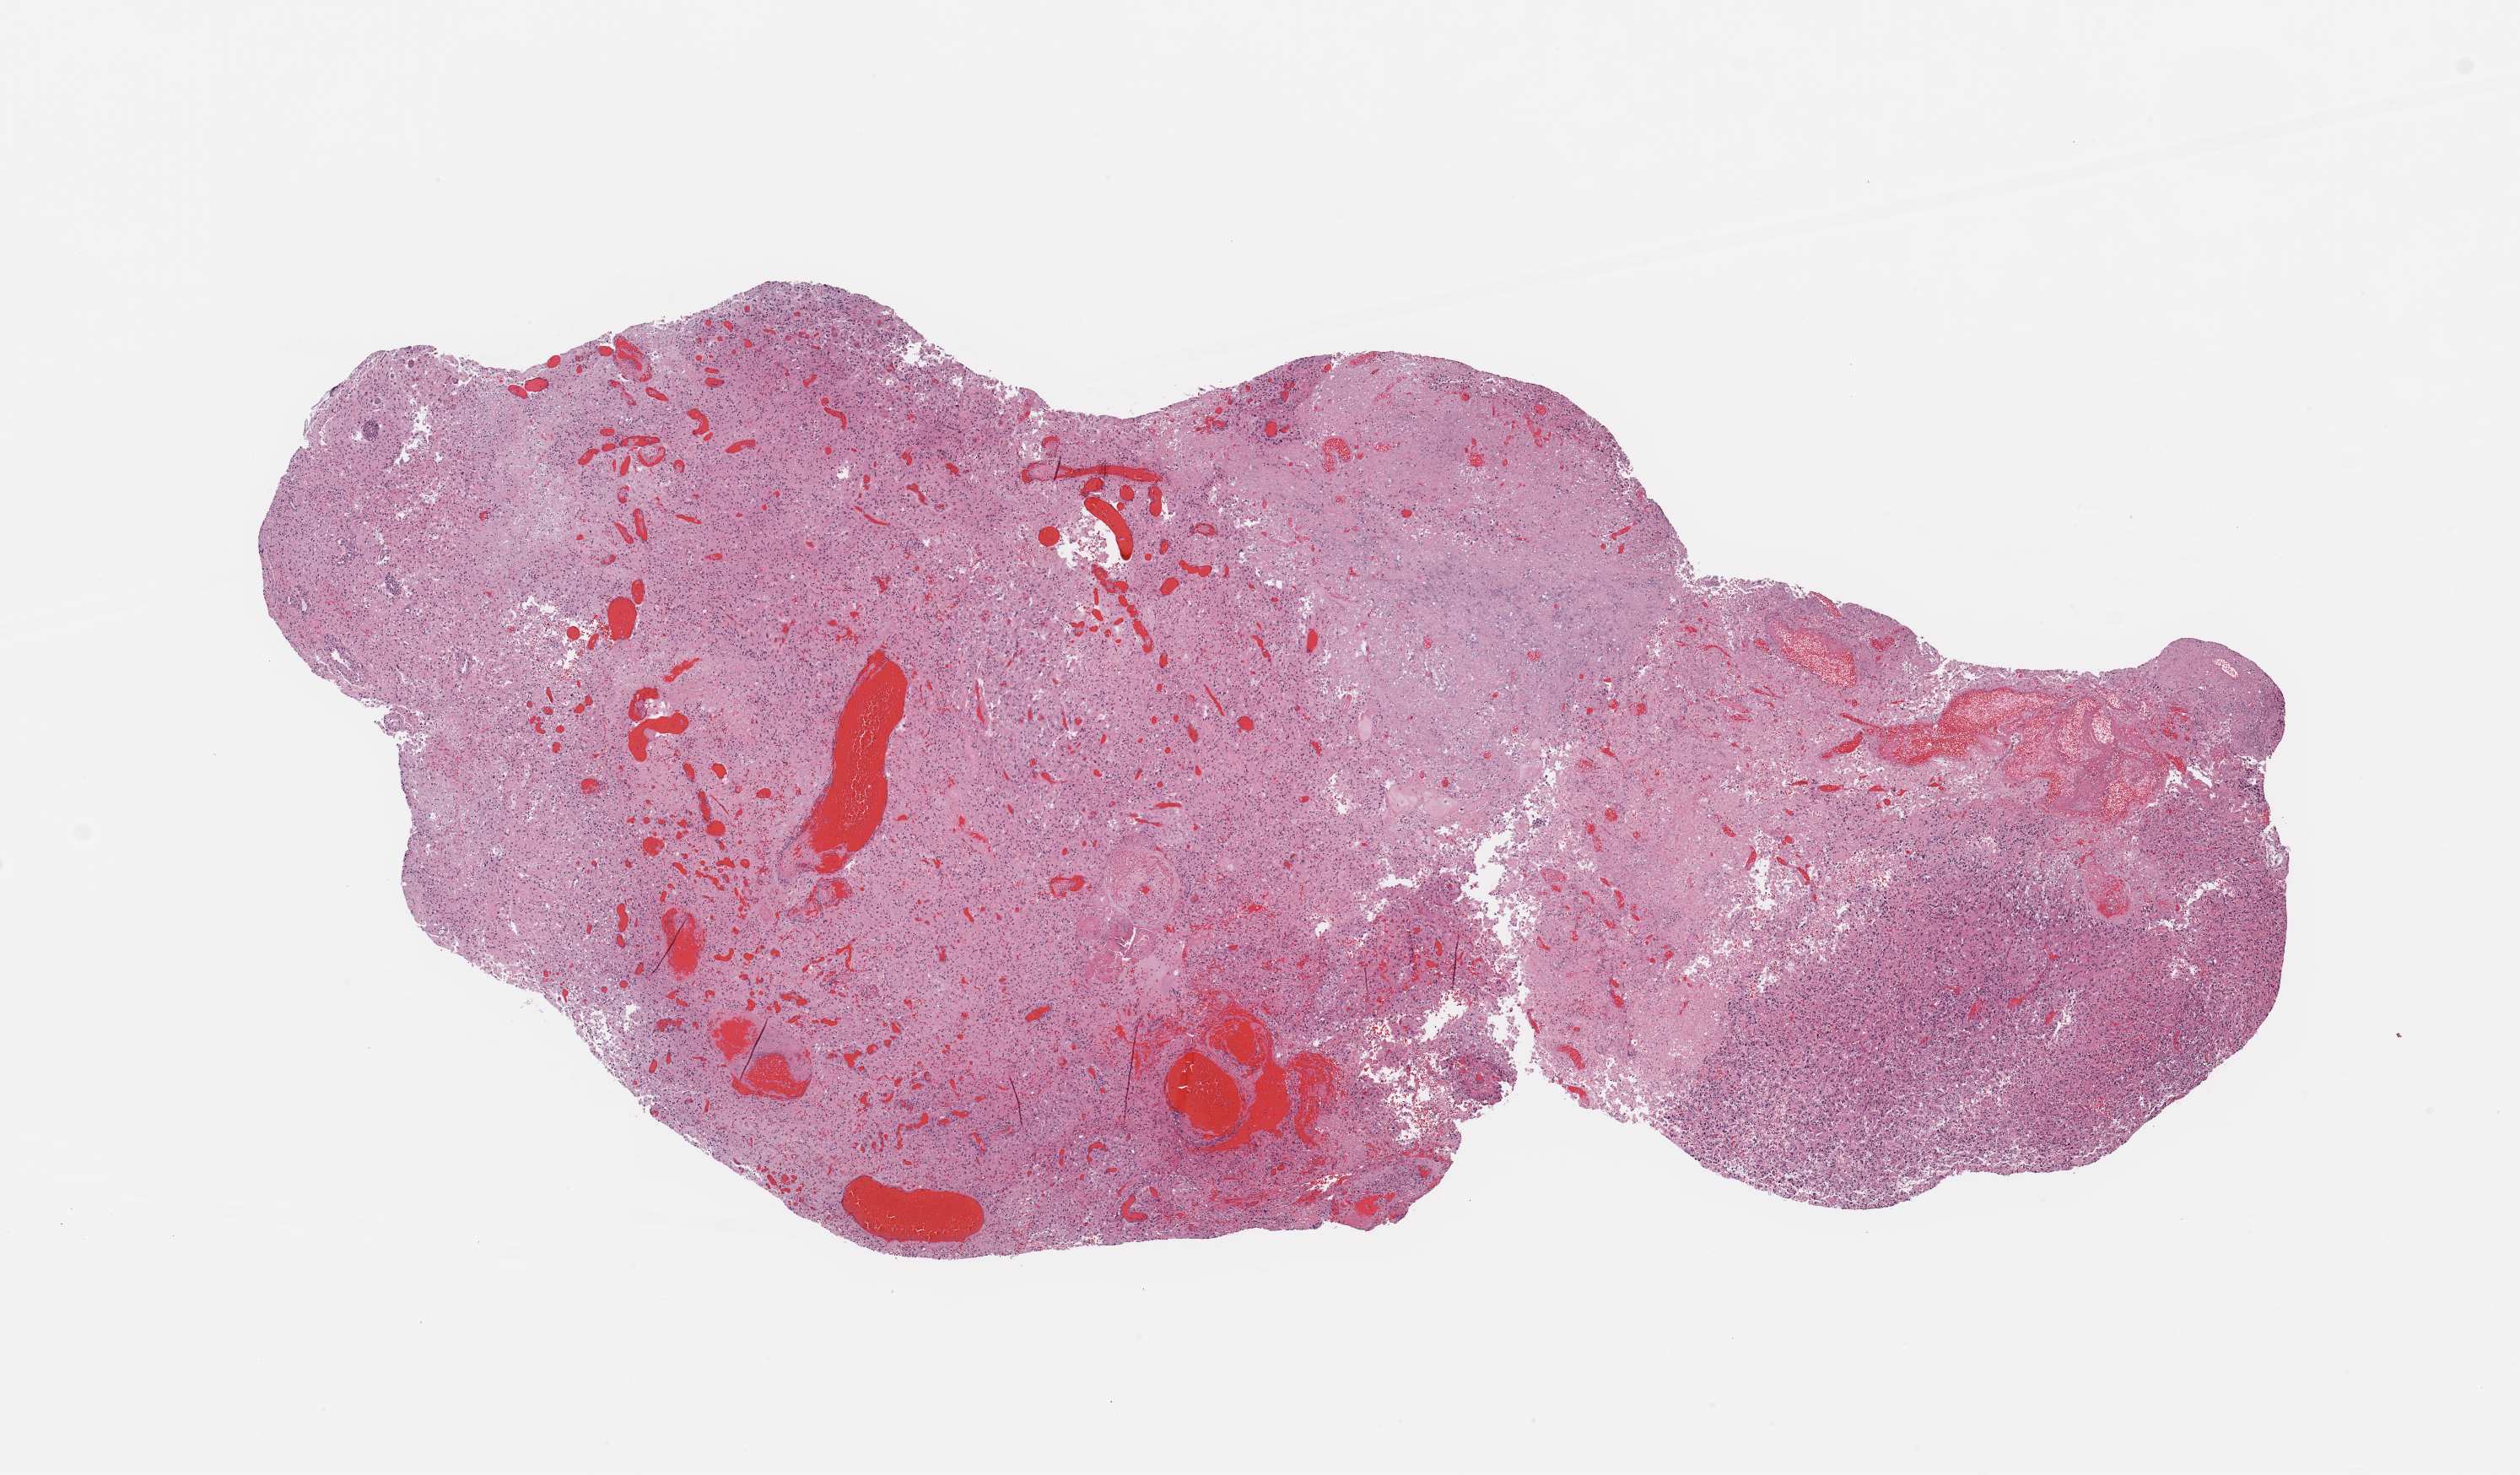
Whole-slide histology image, Hematoxylin and eosin (H&E) stained, low-resolution overview of the scanned area, about 11.8 x 6.9 mm (slide scanned at 20x). Tumour tissue sample, brain. 62-year-old female patient.
Primary tumour site (as recorded): temporal lobe. Diagnosis: Glioblastoma.